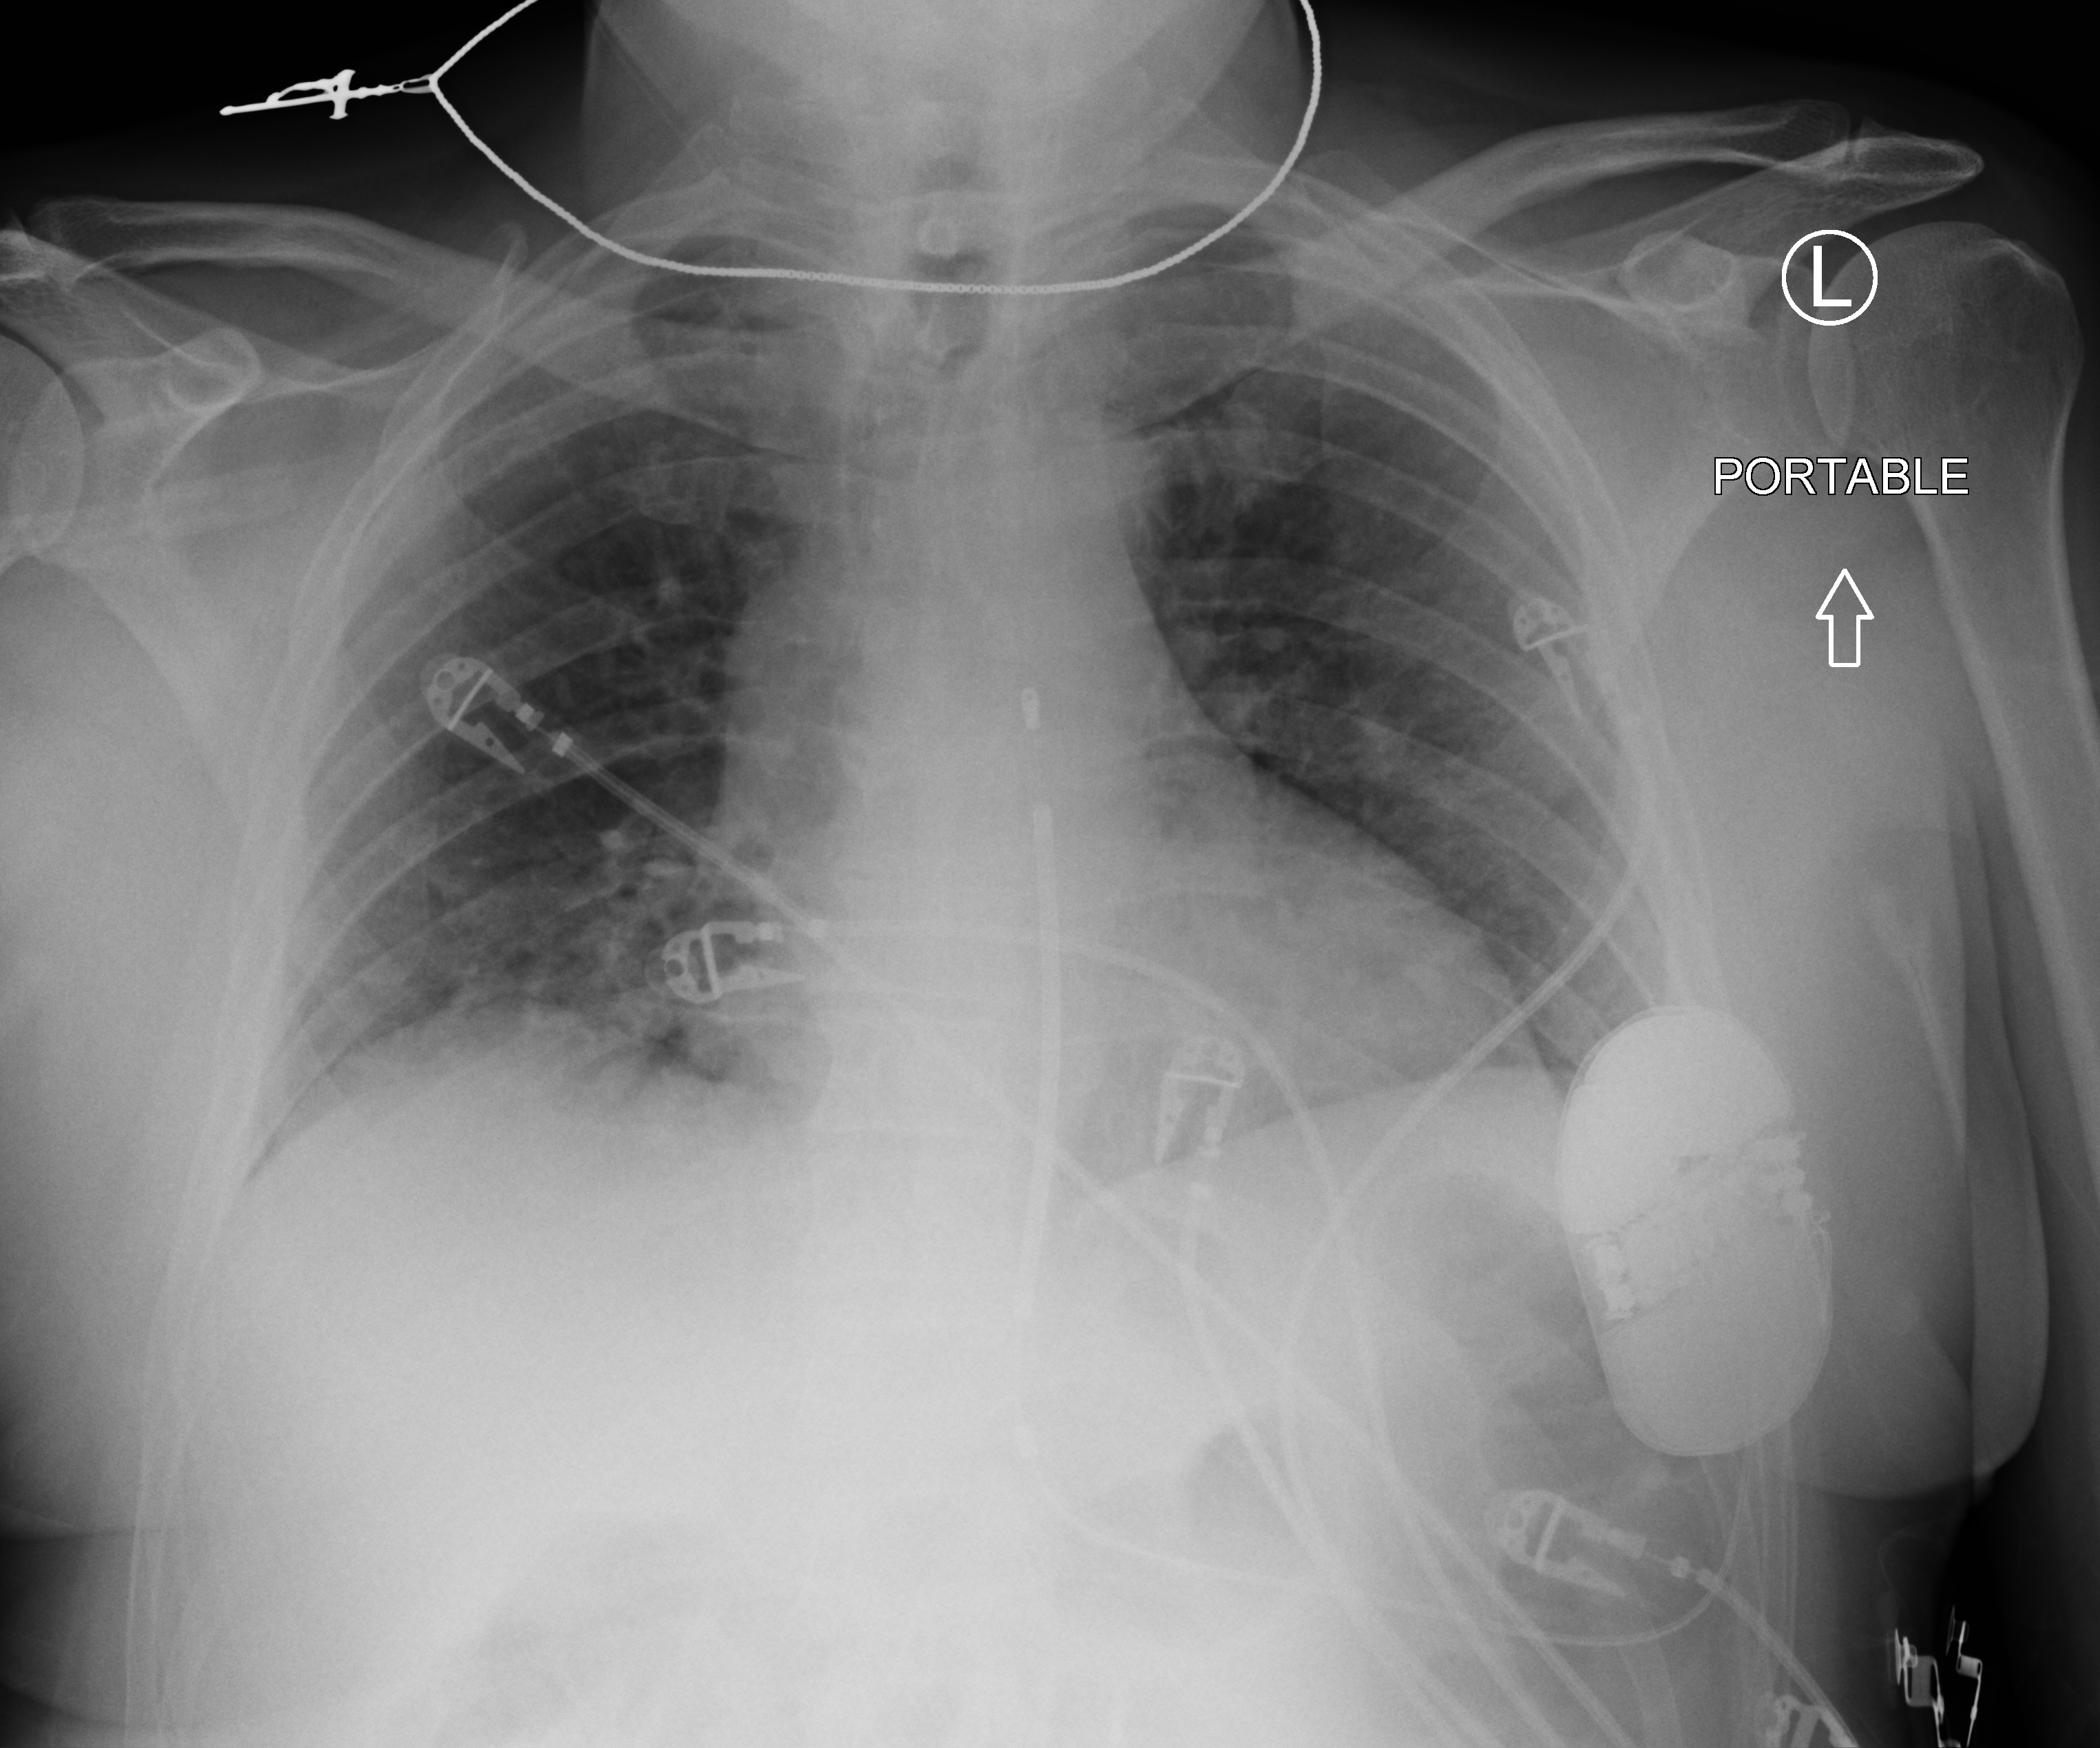
Bedside chest radiograph (computed radiography). Patient hospitalised with COVID-19; male, aged 18–59 years.
Admission-level facts for this patient (not findings on this image; timing relative to this image not recorded):
- COPD (admission record): no
- mechanically ventilated during this hospital stay: no
- length of hospital stay: 19 days